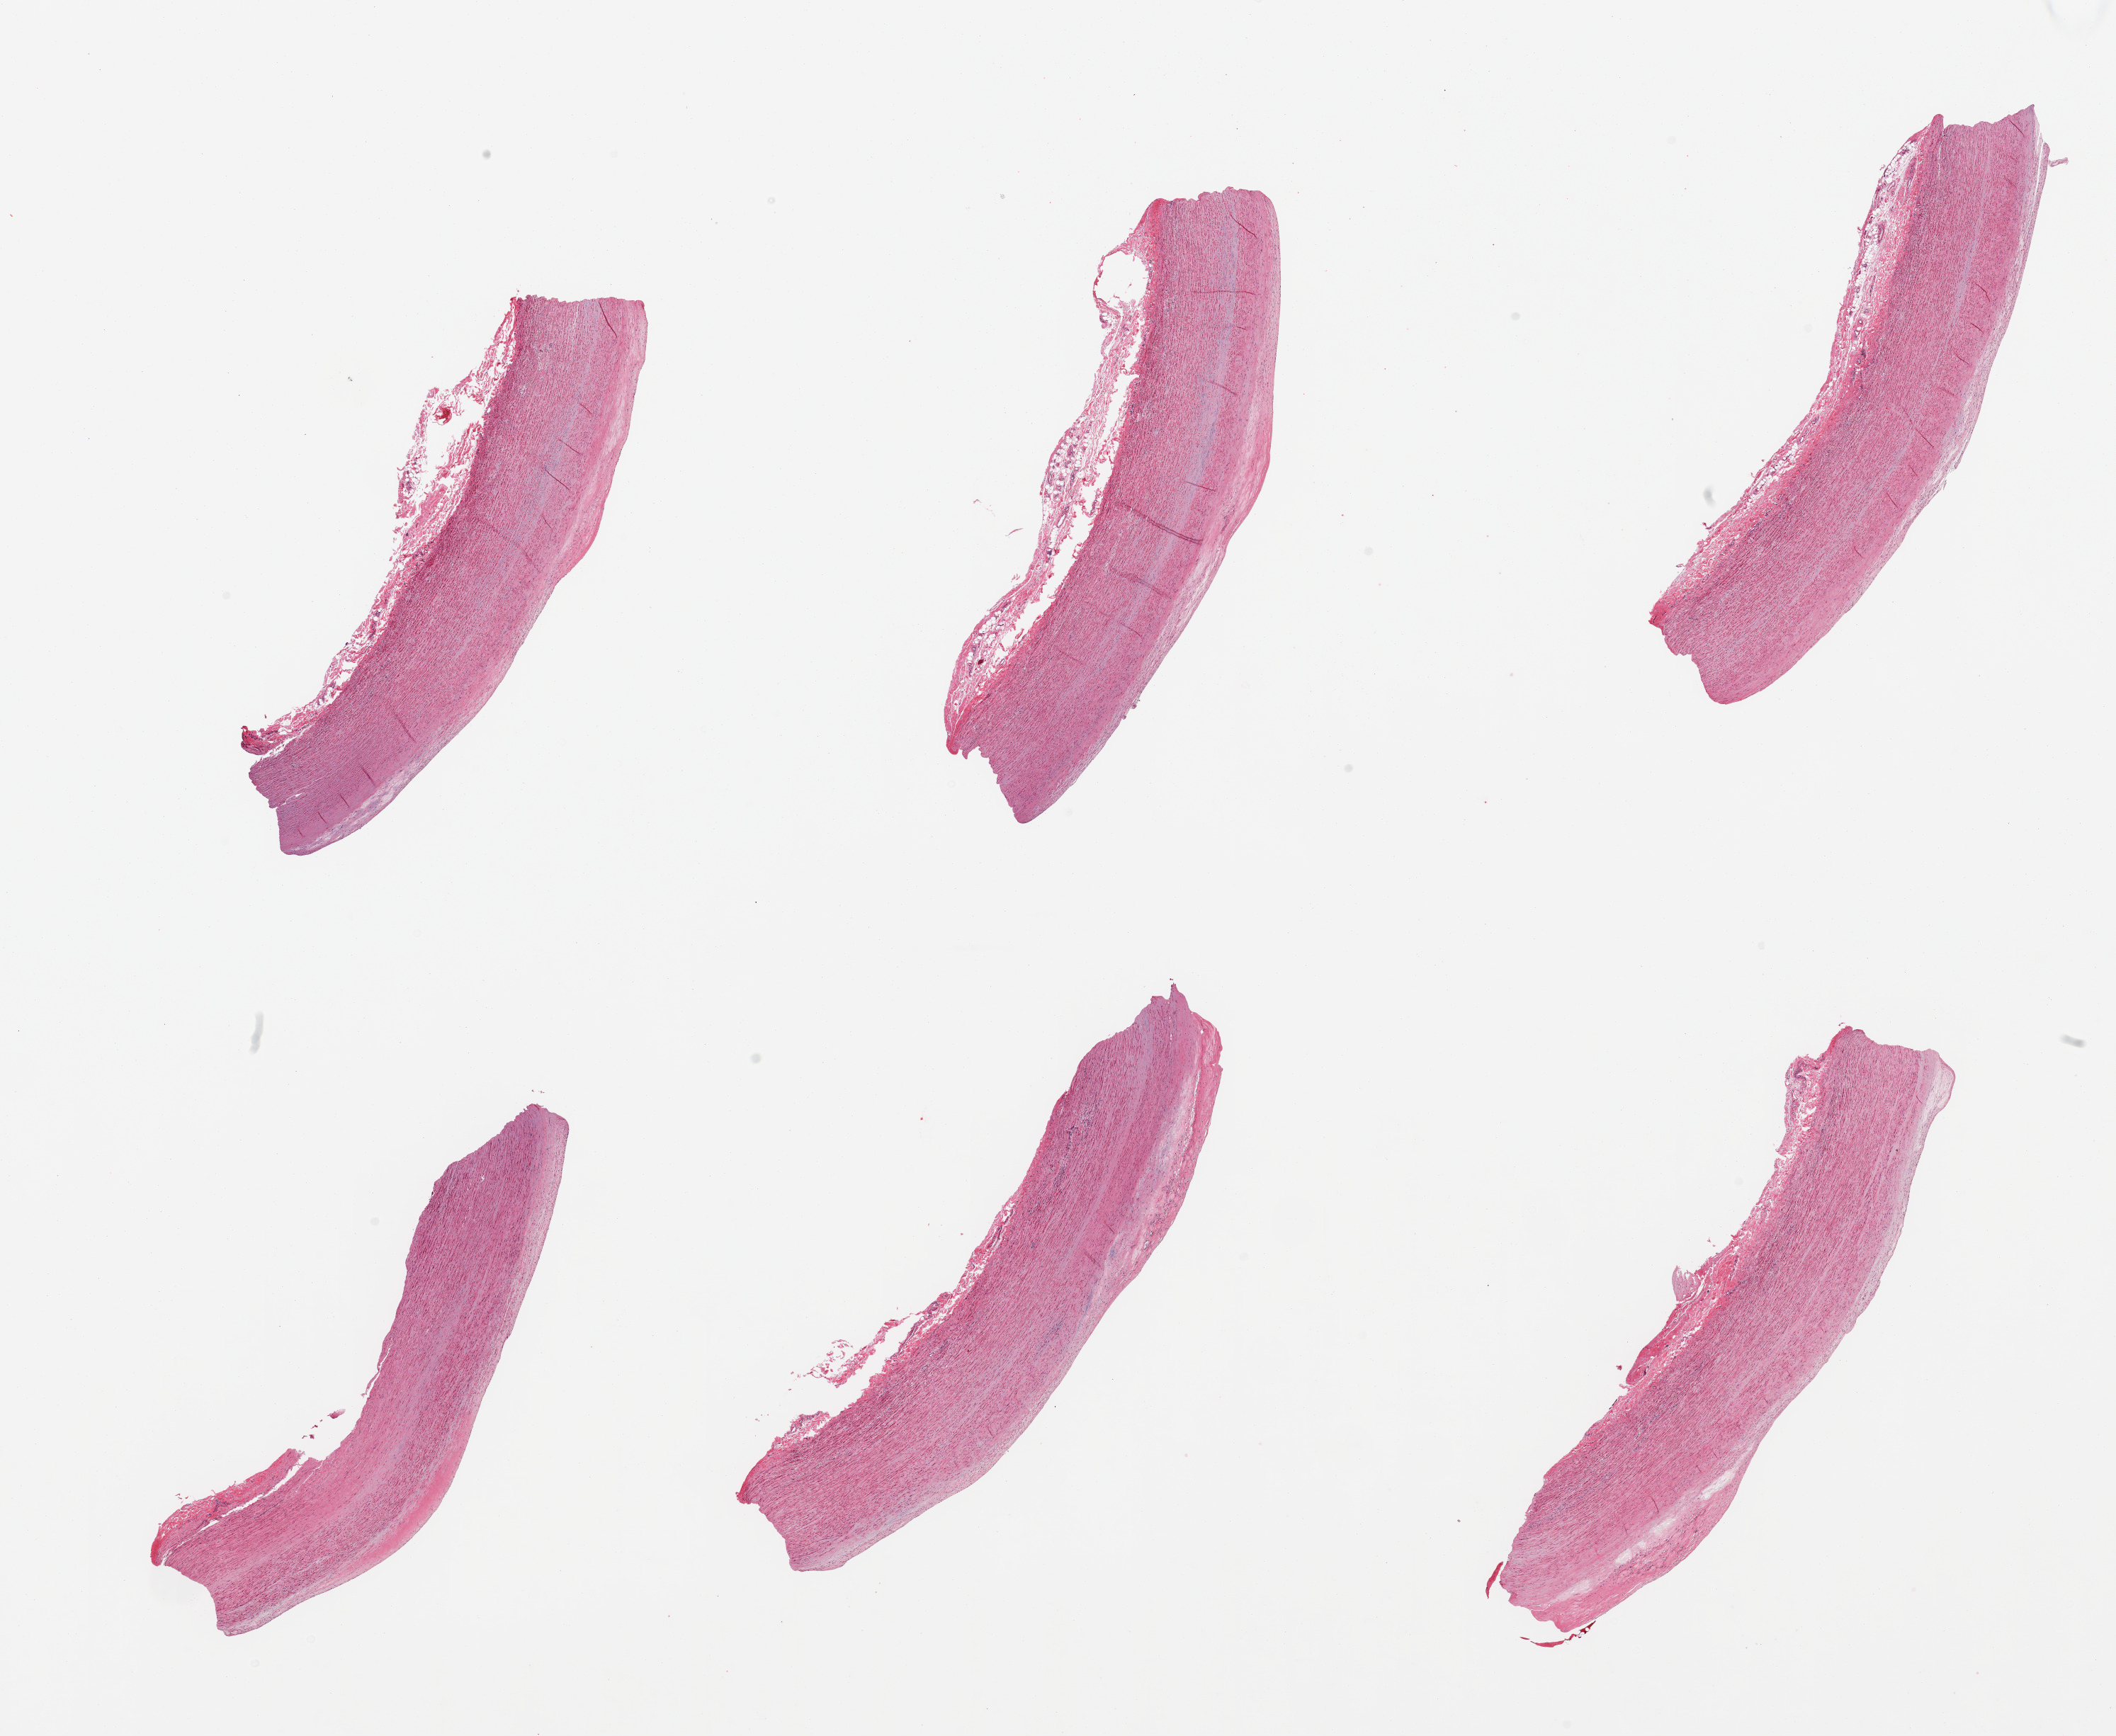
Whole-slide image, hematoxylin and eosin (H&E) stain, shown as a low-resolution overview of the whole scanned area (about 23.6 x 19.4 mm). PAXgene-fixed, paraffin-embedded tissue. Target tissue: aorta. Tissue donor sample. Male donor.
Review note (as recorded): 6 pieces; mild flat sclerotic plaques up to 0.5mm thick.